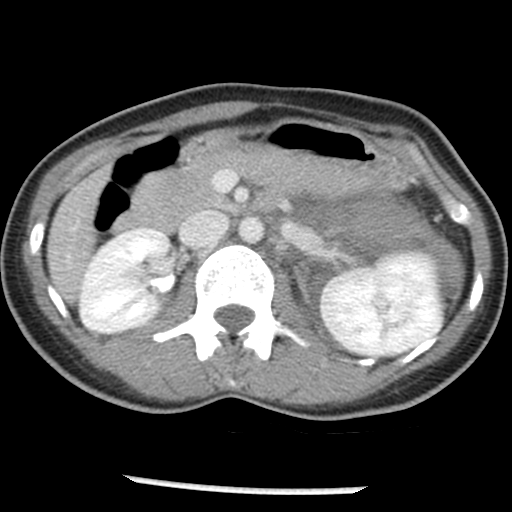
Contrast-enhanced abdominal CT, one axial slice. Slice 23 of 54 in the series (ordered by position). Reconstruction kernel STANDARD. Intravenous contrast given. Soft-tissue window (W 400 / L 40 HU). 512 × 512 image matrix, field of view 240 × 240 mm. Female patient, age 33 years. From the clinical record (not read from this slice): diagnosis: adrenocortical carcinoma; tumour side: left adrenal; tumour size at pathology: 11 cm; Ki-67 index: 20 %; stage (as recorded): 2.
Annotated regions visible in this slice (semi-automatic segmentation, software-assisted and operator-edited):
- mass: bounding box [x1, y1, x2, y2] px = [326, 197, 459, 297]